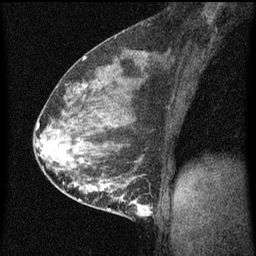
Breast MRI (dynamic contrast-enhanced), one sagittal slice; slice 33 of 60 in the series (ordered by position); dynamic contrast-enhanced series, image 2 of 3 at this slice position (ordered by acquisition); 1.5 T; TE 4.2 ms, TR 8 ms; 2 mm slice thickness; 256 × 256 image matrix. Patient: female, 35 years.
Structures marked on this image (semi-automatically segmented with operator editing):
- analysis volume of interest (the breast-tissue region the enhancement analysis was run in; not a lesion): box from (x=110, y=178) to (x=156, y=219) px
- tumour enhancement mask (voxels above the 70 % enhancement threshold inside the analysis volume of interest): (x=110, y=180)–(x=153, y=217)